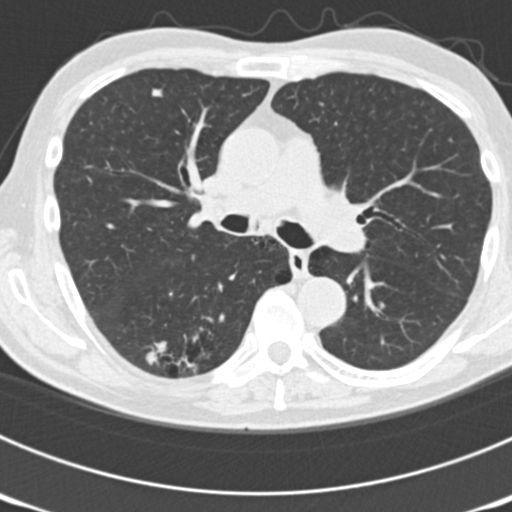
Low-dose screening chest CT, one axial slice; slice 113 of 177 in the series (ordered by position); reconstruction kernel B30f; 120 kVp; lung window (W 1500 / L -600 HU); 2 mm slice thickness; 512 × 512 image matrix, field of view 300 × 300 mm.
Annotated regions visible in this slice (outlined manually by an expert reader):
- lesion 1 (nodule, upper lobe of right lung): bounding box [x1, y1, x2, y2] px = [151, 88, 164, 98]